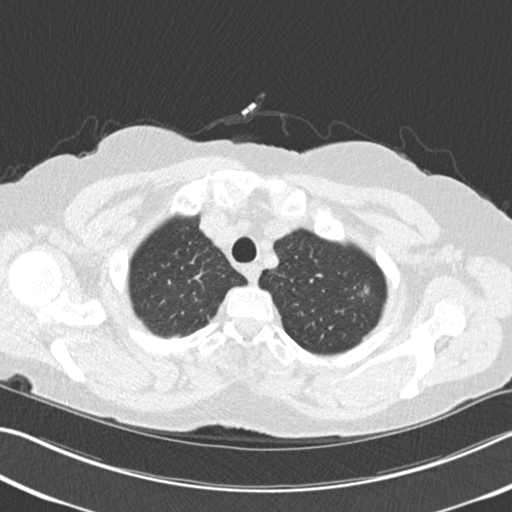
Low-dose screening chest CT, one axial slice; position 197 of 225 along the scan axis; reconstruction kernel B30f; lung window (W 1500 / L -600 HU); 512 × 512 image matrix.
Structures marked on this image (outlined manually by an expert reader):
- lesion 1 (tumor): bounding box <362,286,369,295> (left, top, right, bottom; pixels)